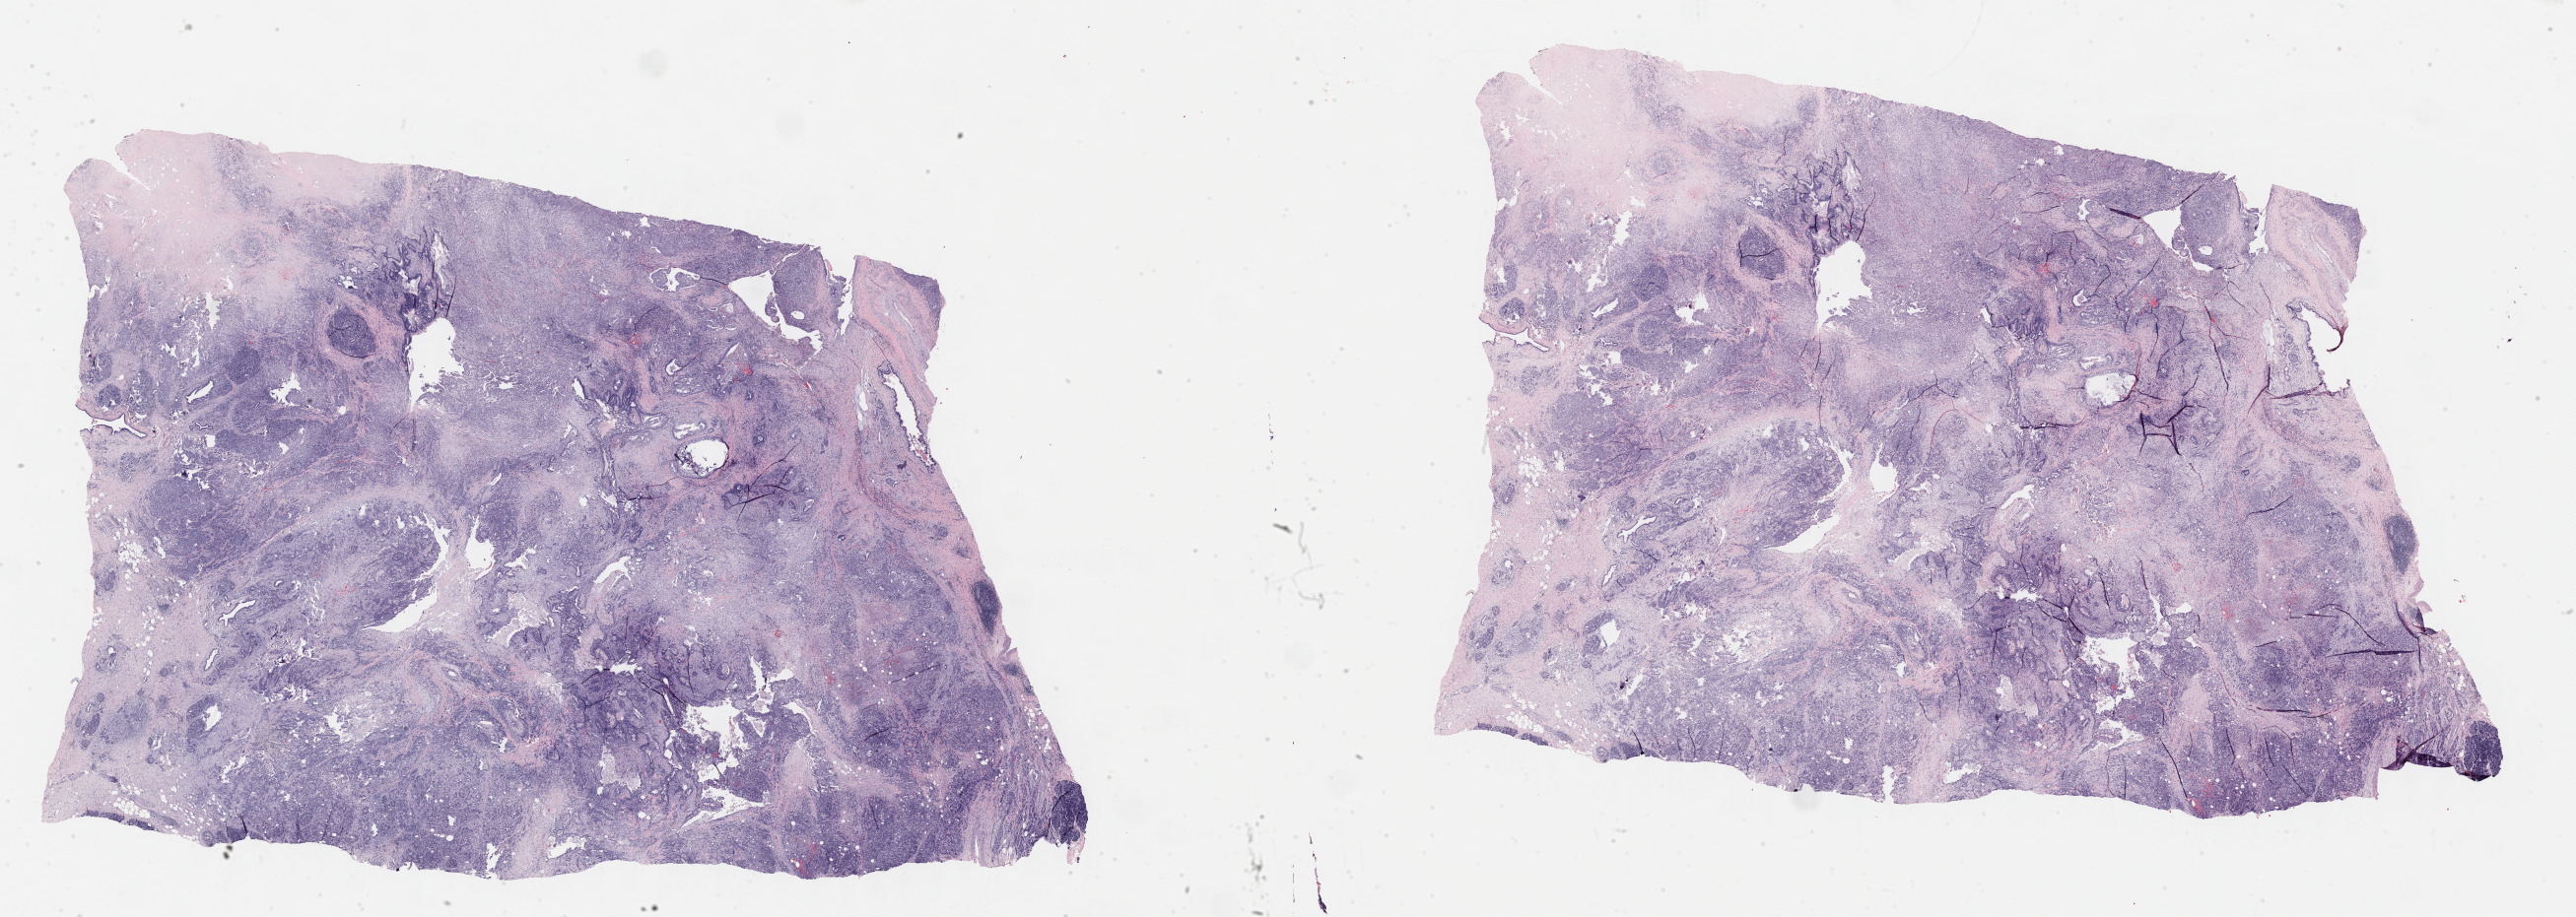
H&E whole-slide image, low-resolution overview of the scanned area, about 42.3 x 15.1 mm (acquisition: 40x scan); formalin-fixed paraffin-embedded (FFPE) diagnostic section; primary tumour sample from the pancreas. Female patient; age at initial diagnosis 48 years. Histologic grade: G3 (poorly differentiated).
Lymph nodes positive (case pathology): 2 of 11 examined. Histologic diagnosis: Infiltrating duct carcinoma, NOS (head of pancreas). AJCC pathologic stage: IIB (7th edition).